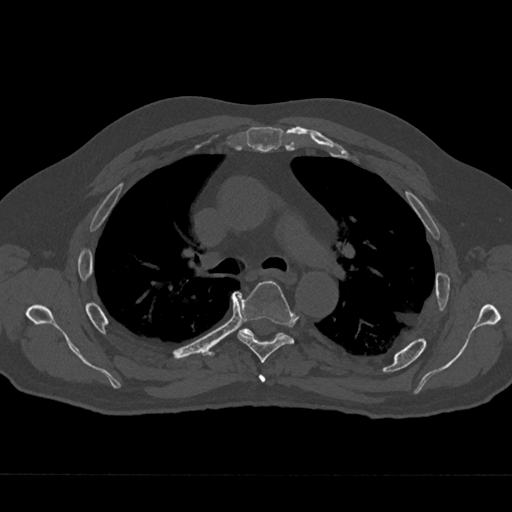
CT including the spine, one axial slice; slice 464 of 797 in the series (ordered by position); bone window (W 1800 / L 400 HU); 0.5 mm slice thickness; 512 × 512 image matrix, field of view 377 × 377 mm. Male patient, age 75 years. From the clinical record (not read from this slice): primary cancer: renal; vertebrae with lytic lesions (as recorded): T4.
Outlined on this slice (semi-automatic segmentation, software-assisted and operator-edited):
- T4 vertebra: box from (x=258, y=374) to (x=266, y=382) px
- T5 vertebra: (x=237, y=281)–(x=294, y=363)
- T6 vertebra: (x=240, y=328)–(x=282, y=337)